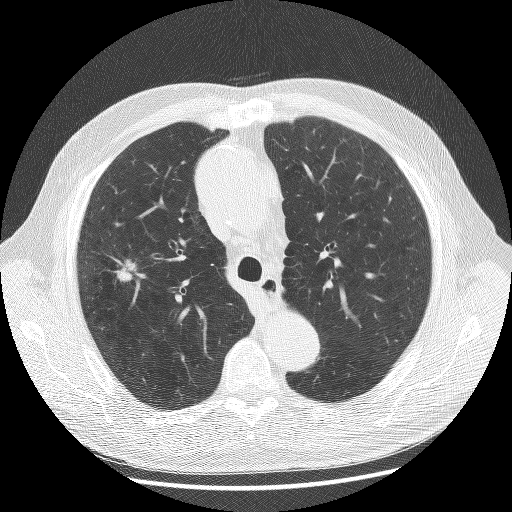
Chest CT (low-dose screening protocol), one axial image, baseline annual screen, lung window (W 1500 / L -600 HU), 2.5 mm slice thickness, 120 kVp, slice 47 of 175 in the series. Male participant, aged 70 years at enrolment. Current smoker at enrolment.
Expert reader's lesion annotation, bounding box <74,239,149,307> (left, top, right, bottom; pixels). The screening reader recorded 2 non-calcified nodules or masses ≥4 mm on this exam (left upper lobe, right upper lobe); which of them this box marks is not recorded. Official screen result: positive, change unspecified: nodule(s) >= 4 mm or enlarging nodule(s), mass(es), or other non-specific abnormalities suspicious for lung cancer. Later outcome: lung cancer diagnosed 23 days after this screen — non-small cell carcinoma, right upper lobe, poorly differentiated (G3), stage IA (AJCC 6th edition), 20 mm at pathology.